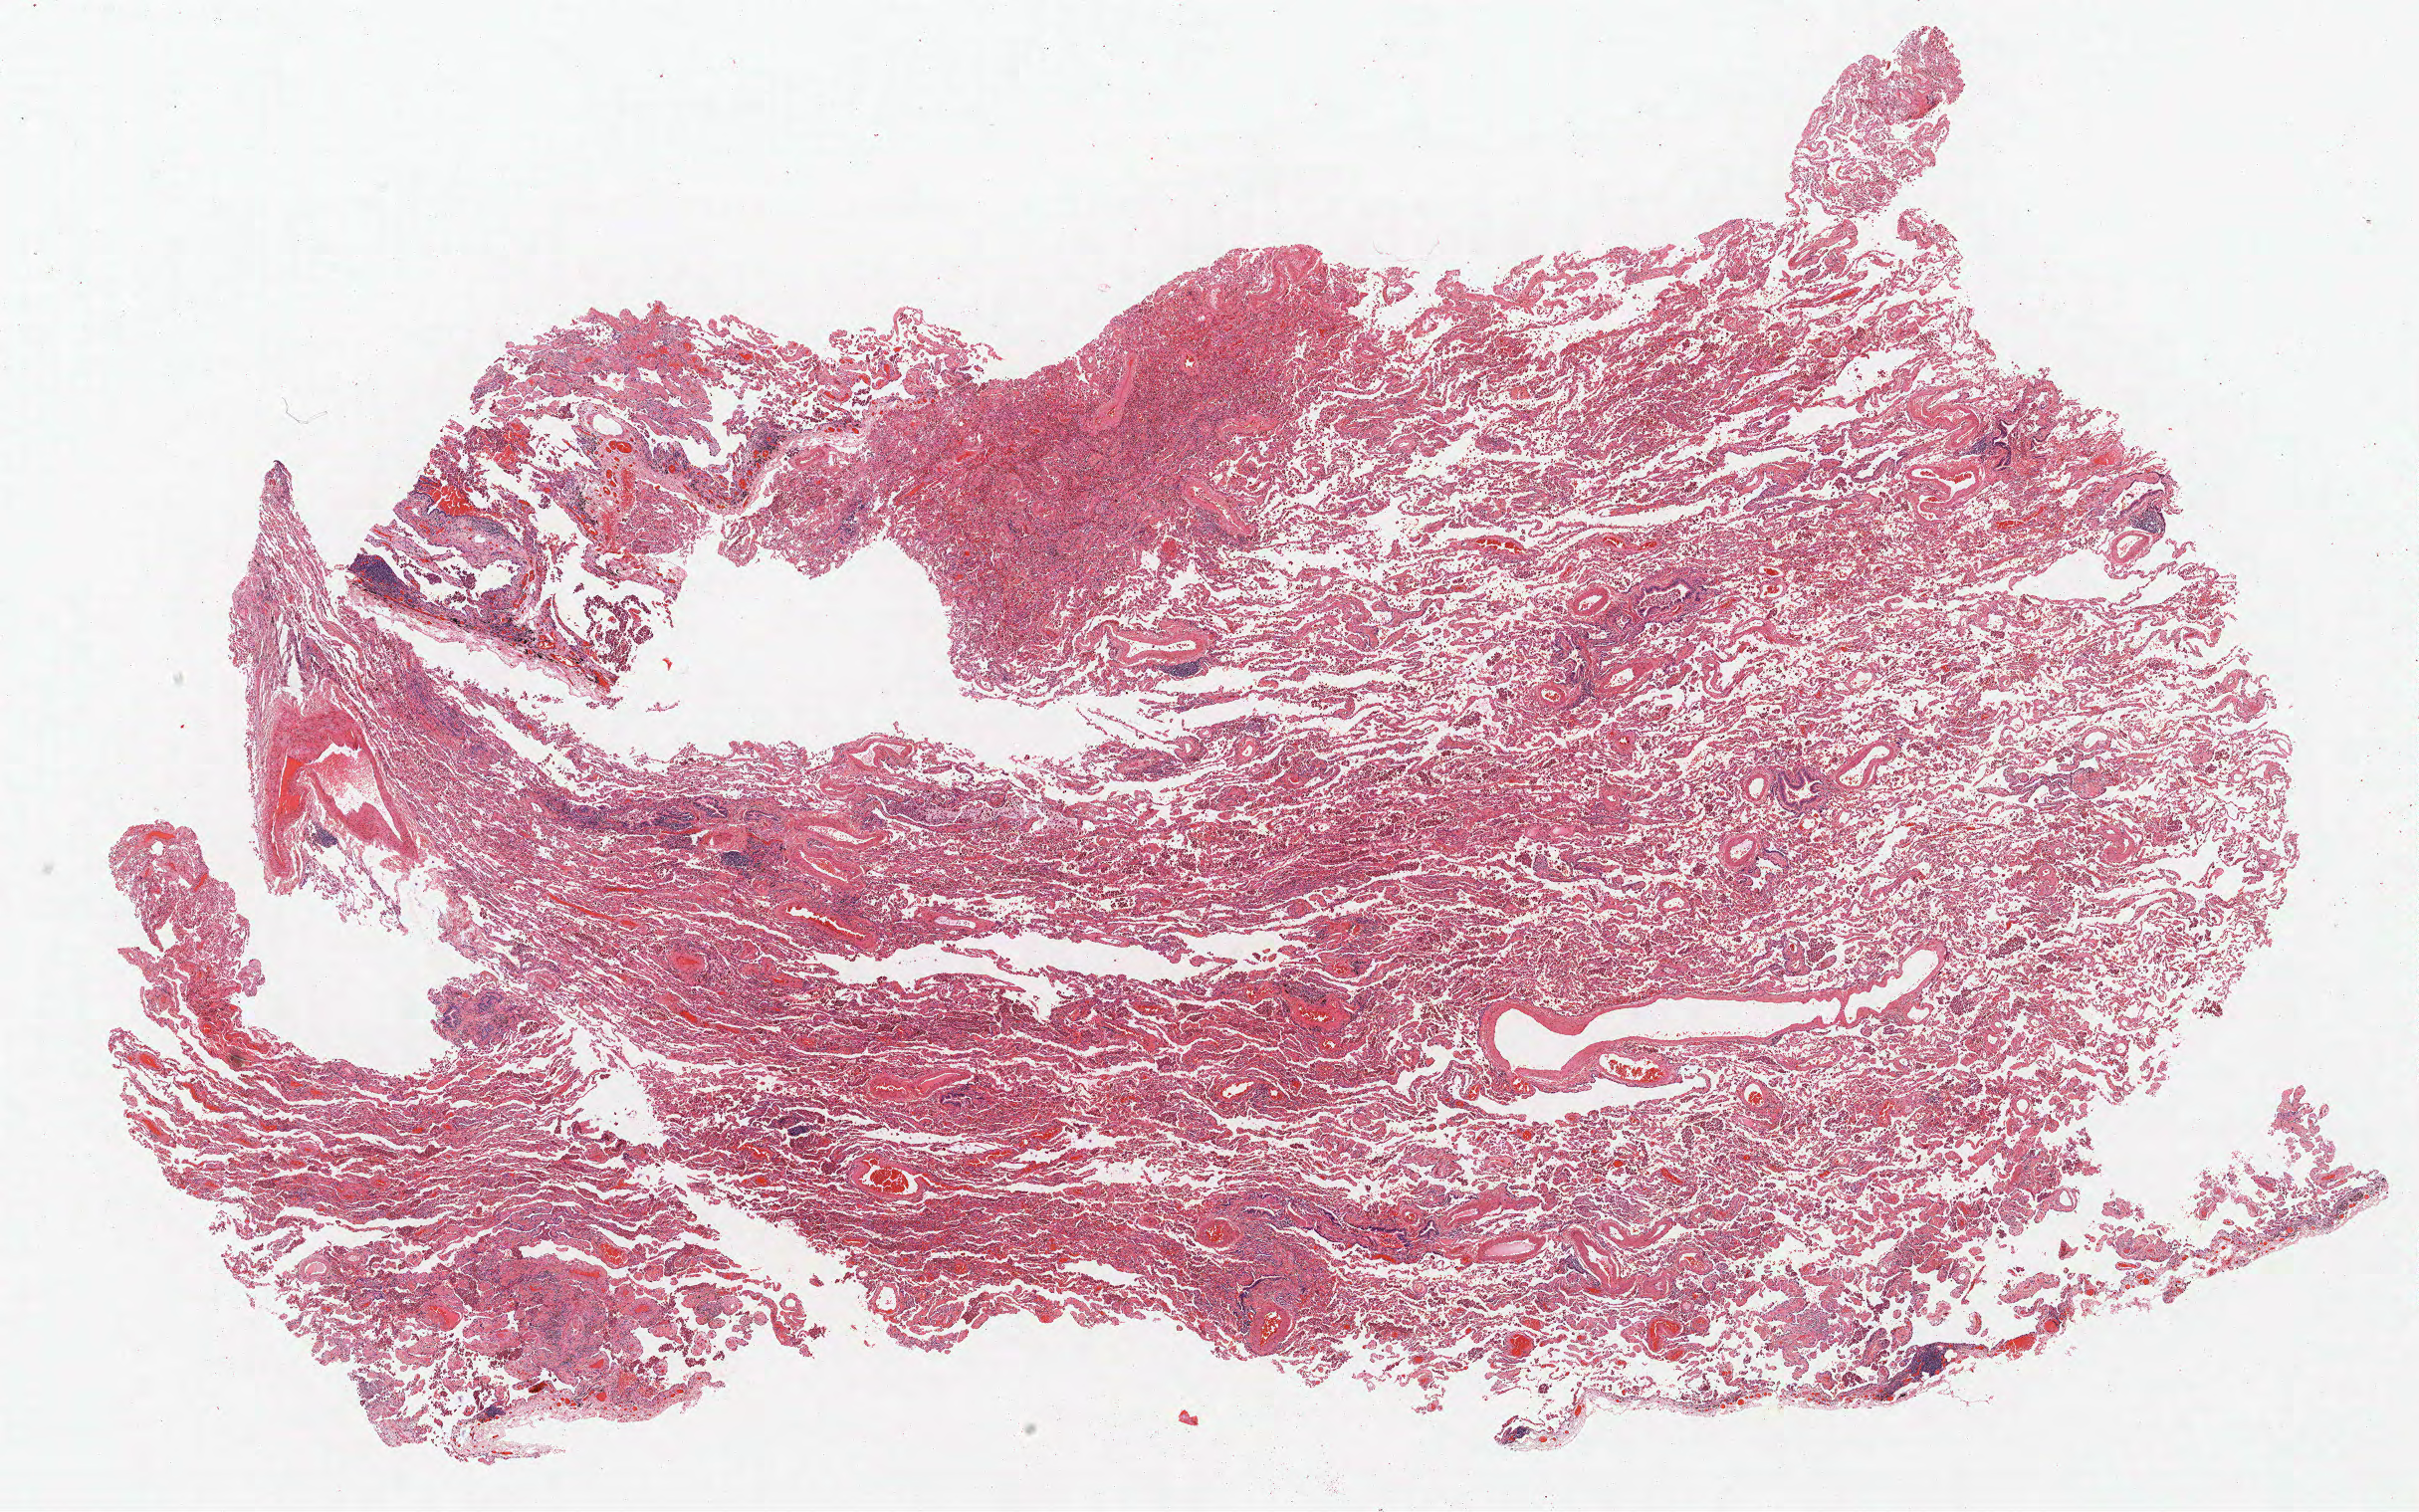
Hematoxylin and eosin (H&E) stained whole-slide image — low-resolution overview of the scanned area, about 19.4 x 12.2 mm. Formalin-fixed paraffin-embedded (FFPE) section. Lung tissue. Male patient, aged 71 at enrolment. Current smoker at enrolment. Grade: moderately differentiated (G2).
* stage (AJCC 6th edition): IA
* tumour size (pathology): 24 mm
* participant's lung-cancer diagnosis: Adenocarcinoma, NOS
* primary tumour location (clinical record): right lower lobe